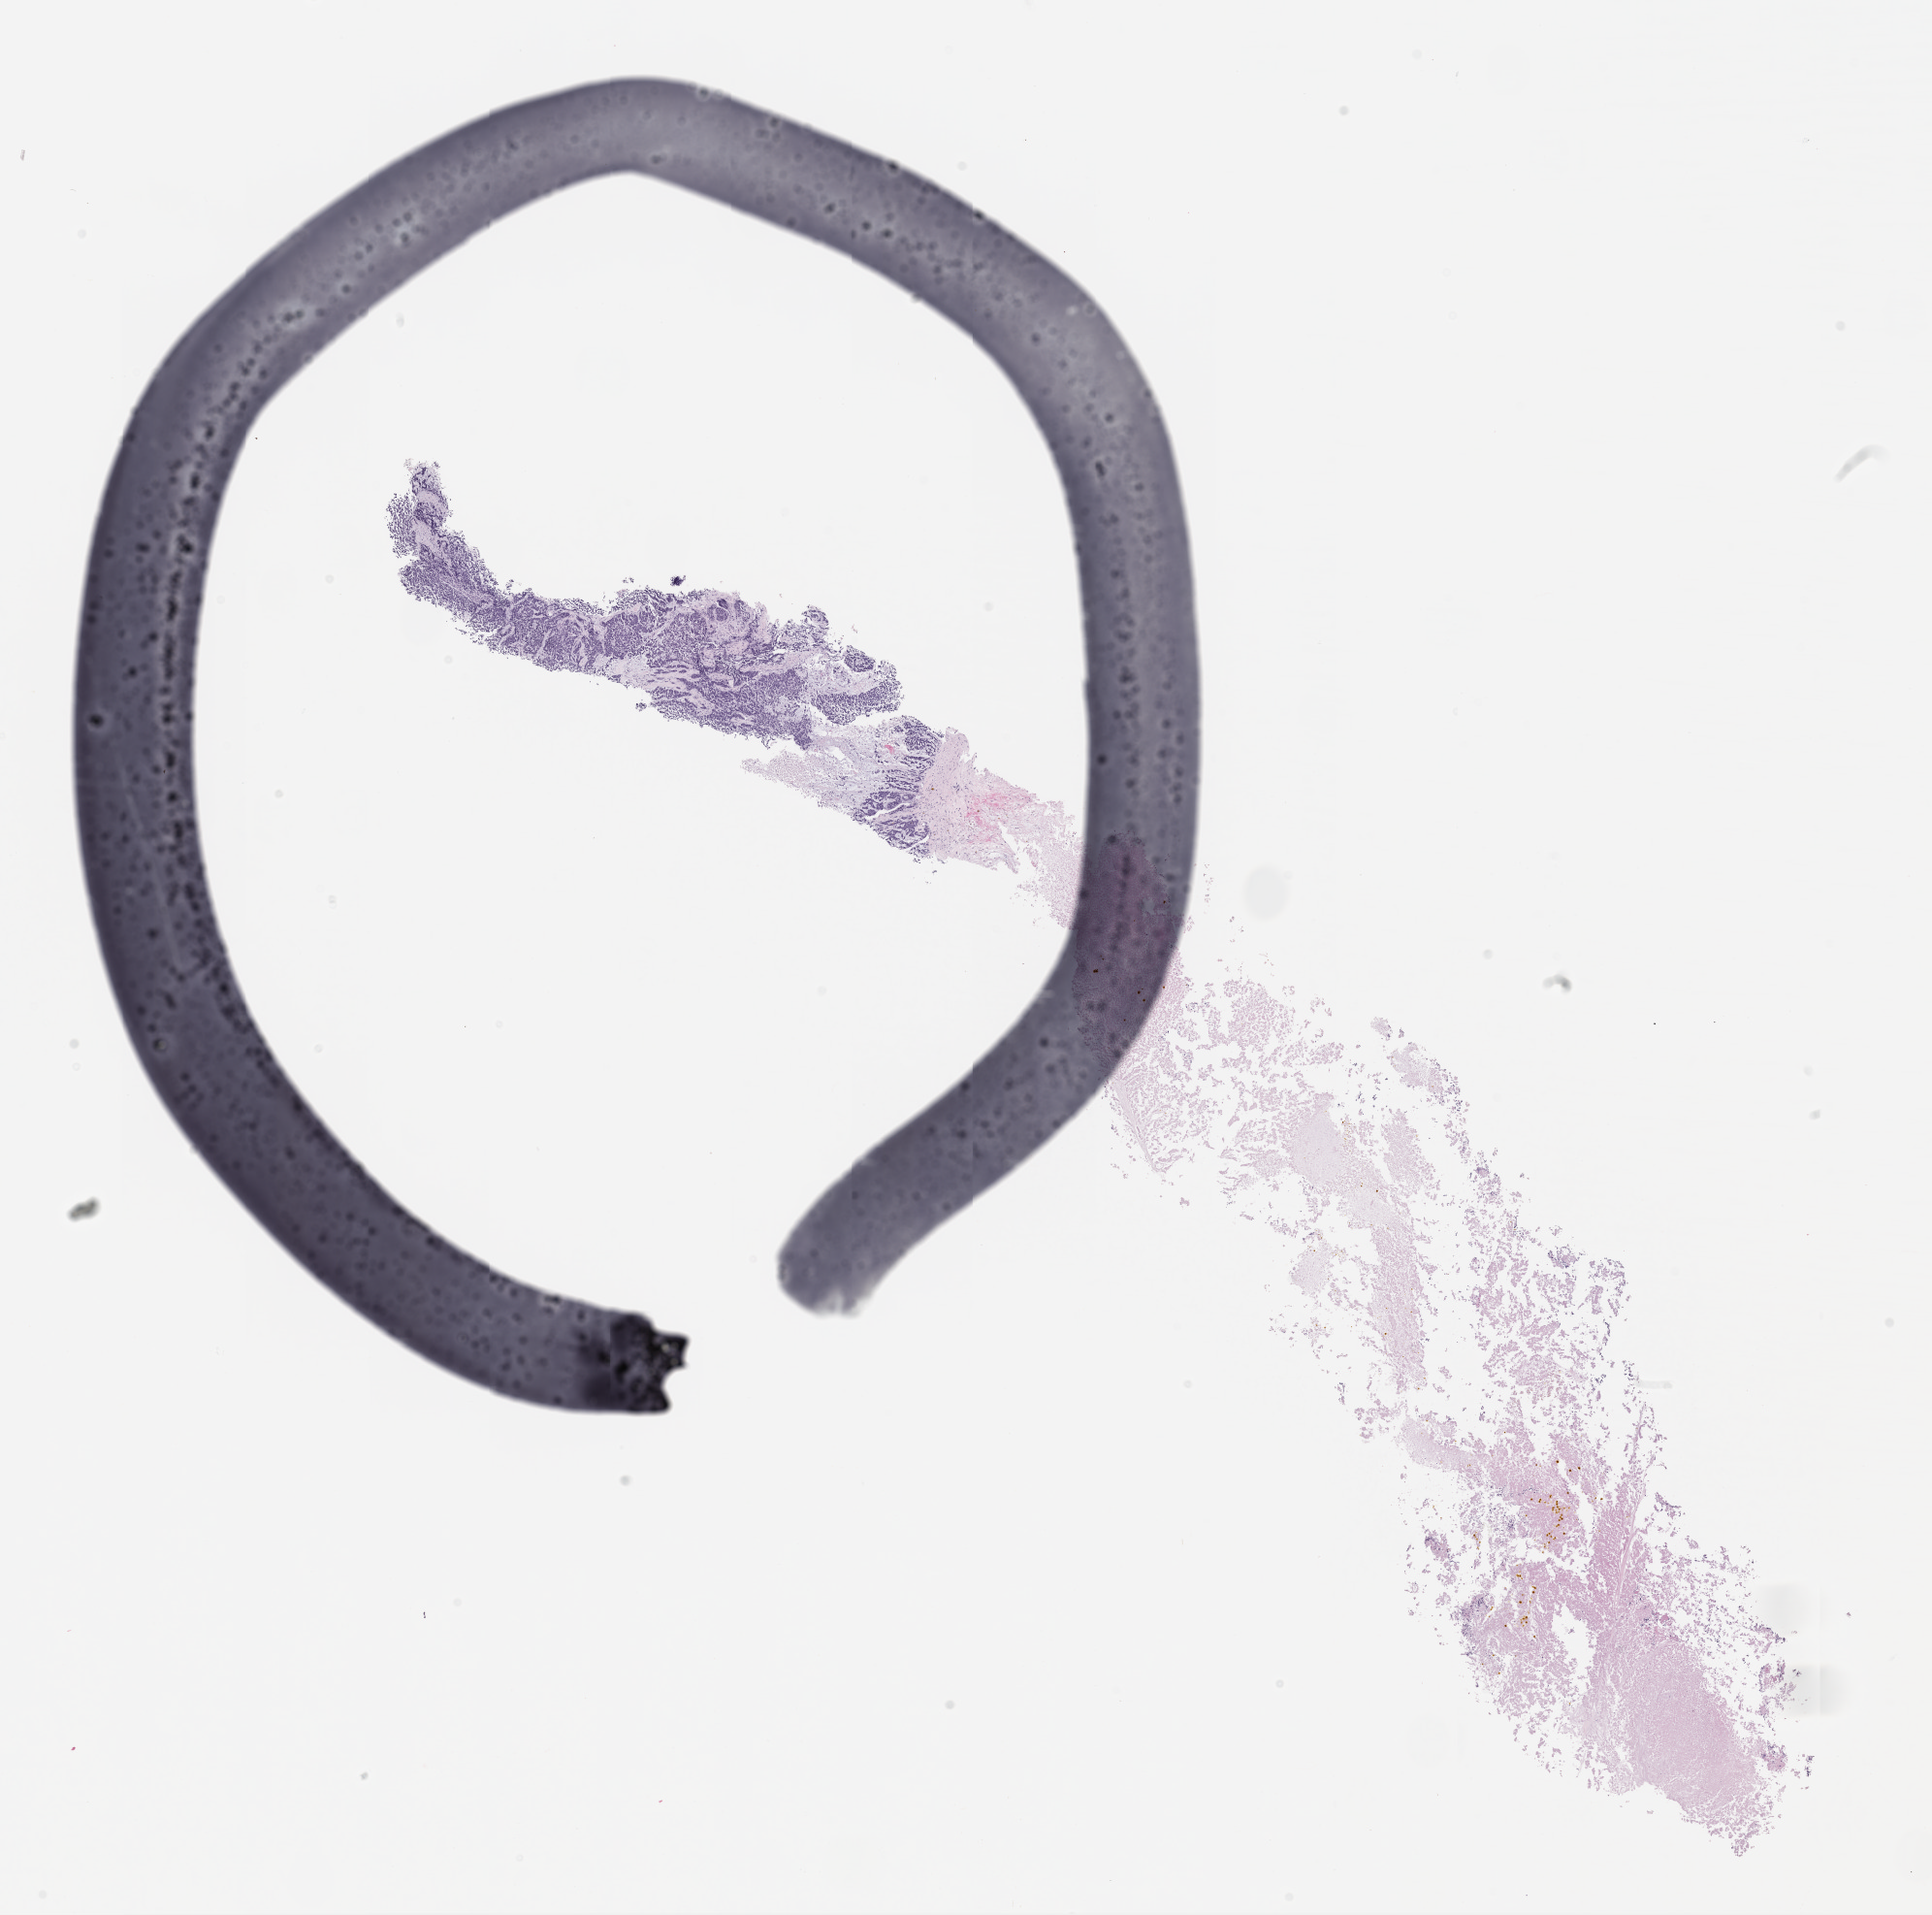
Whole-slide image, hematoxylin and eosin (H&E) stain of the patient's (originator) tumor tissue, whole scanned area (about 16.0 x 15.9 mm) shown as a low-resolution overview; formalin-fixed, paraffin-embedded (FFPE) tissue; tumor site category: ovary. Female patient, aged 54.
• diagnosis: Ovarian Carcinoma